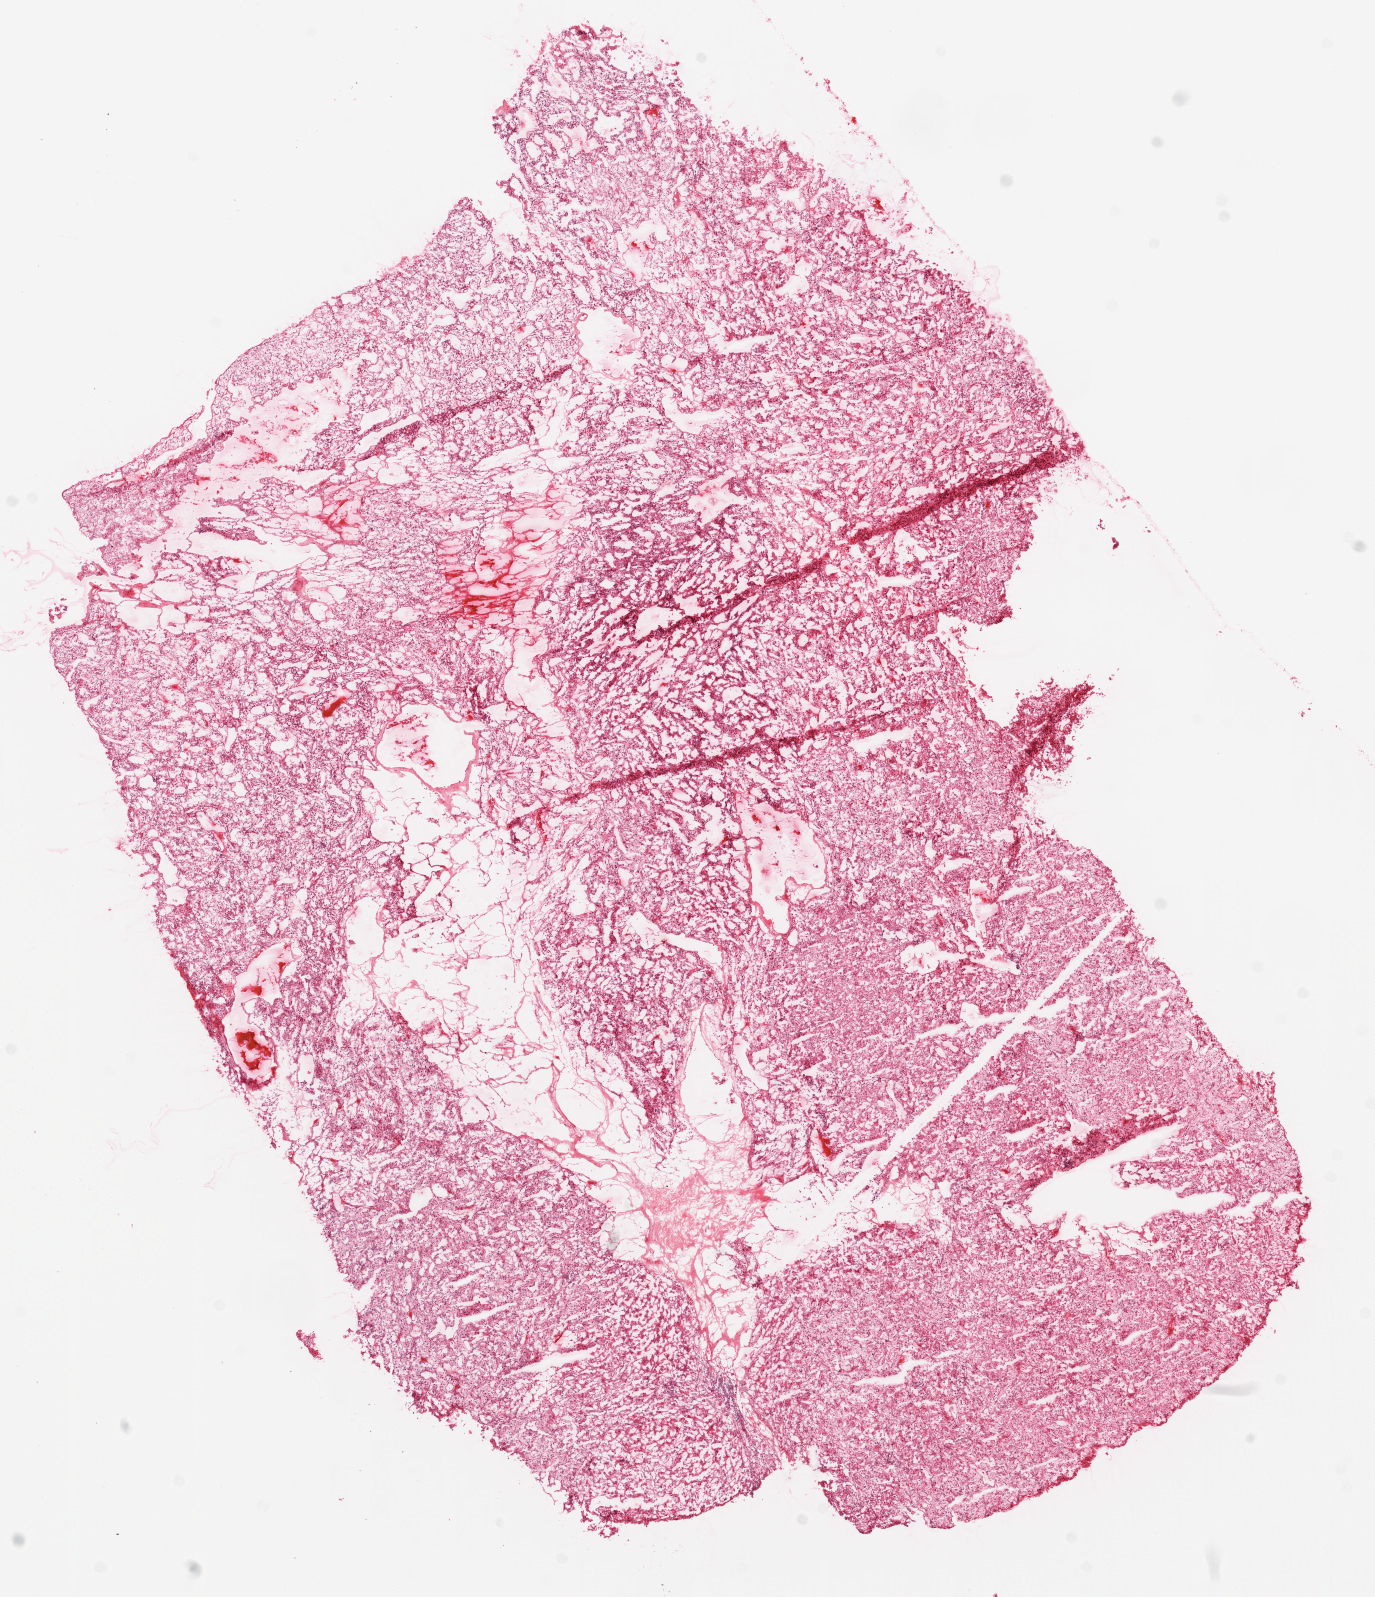
Digitized H&E-stained tissue section (whole slide) — whole scanned area (about 11.0 x 12.8 mm, from a 20x scan) shown as a low-resolution overview, frozen section from the top of the tissue portion, primary tumour sample from the kidney. Patient: male, age at initial diagnosis 55 years. Histologic grade: G2 (moderately differentiated). Slide review estimates, as recorded: tumour cells 85%, tumour nuclei 90%, normal cells 0%, stromal cells 15%, necrosis 0%.
- AJCC pathologic stage: IV (6th edition)
- diagnosis: Clear cell adenocarcinoma, NOS